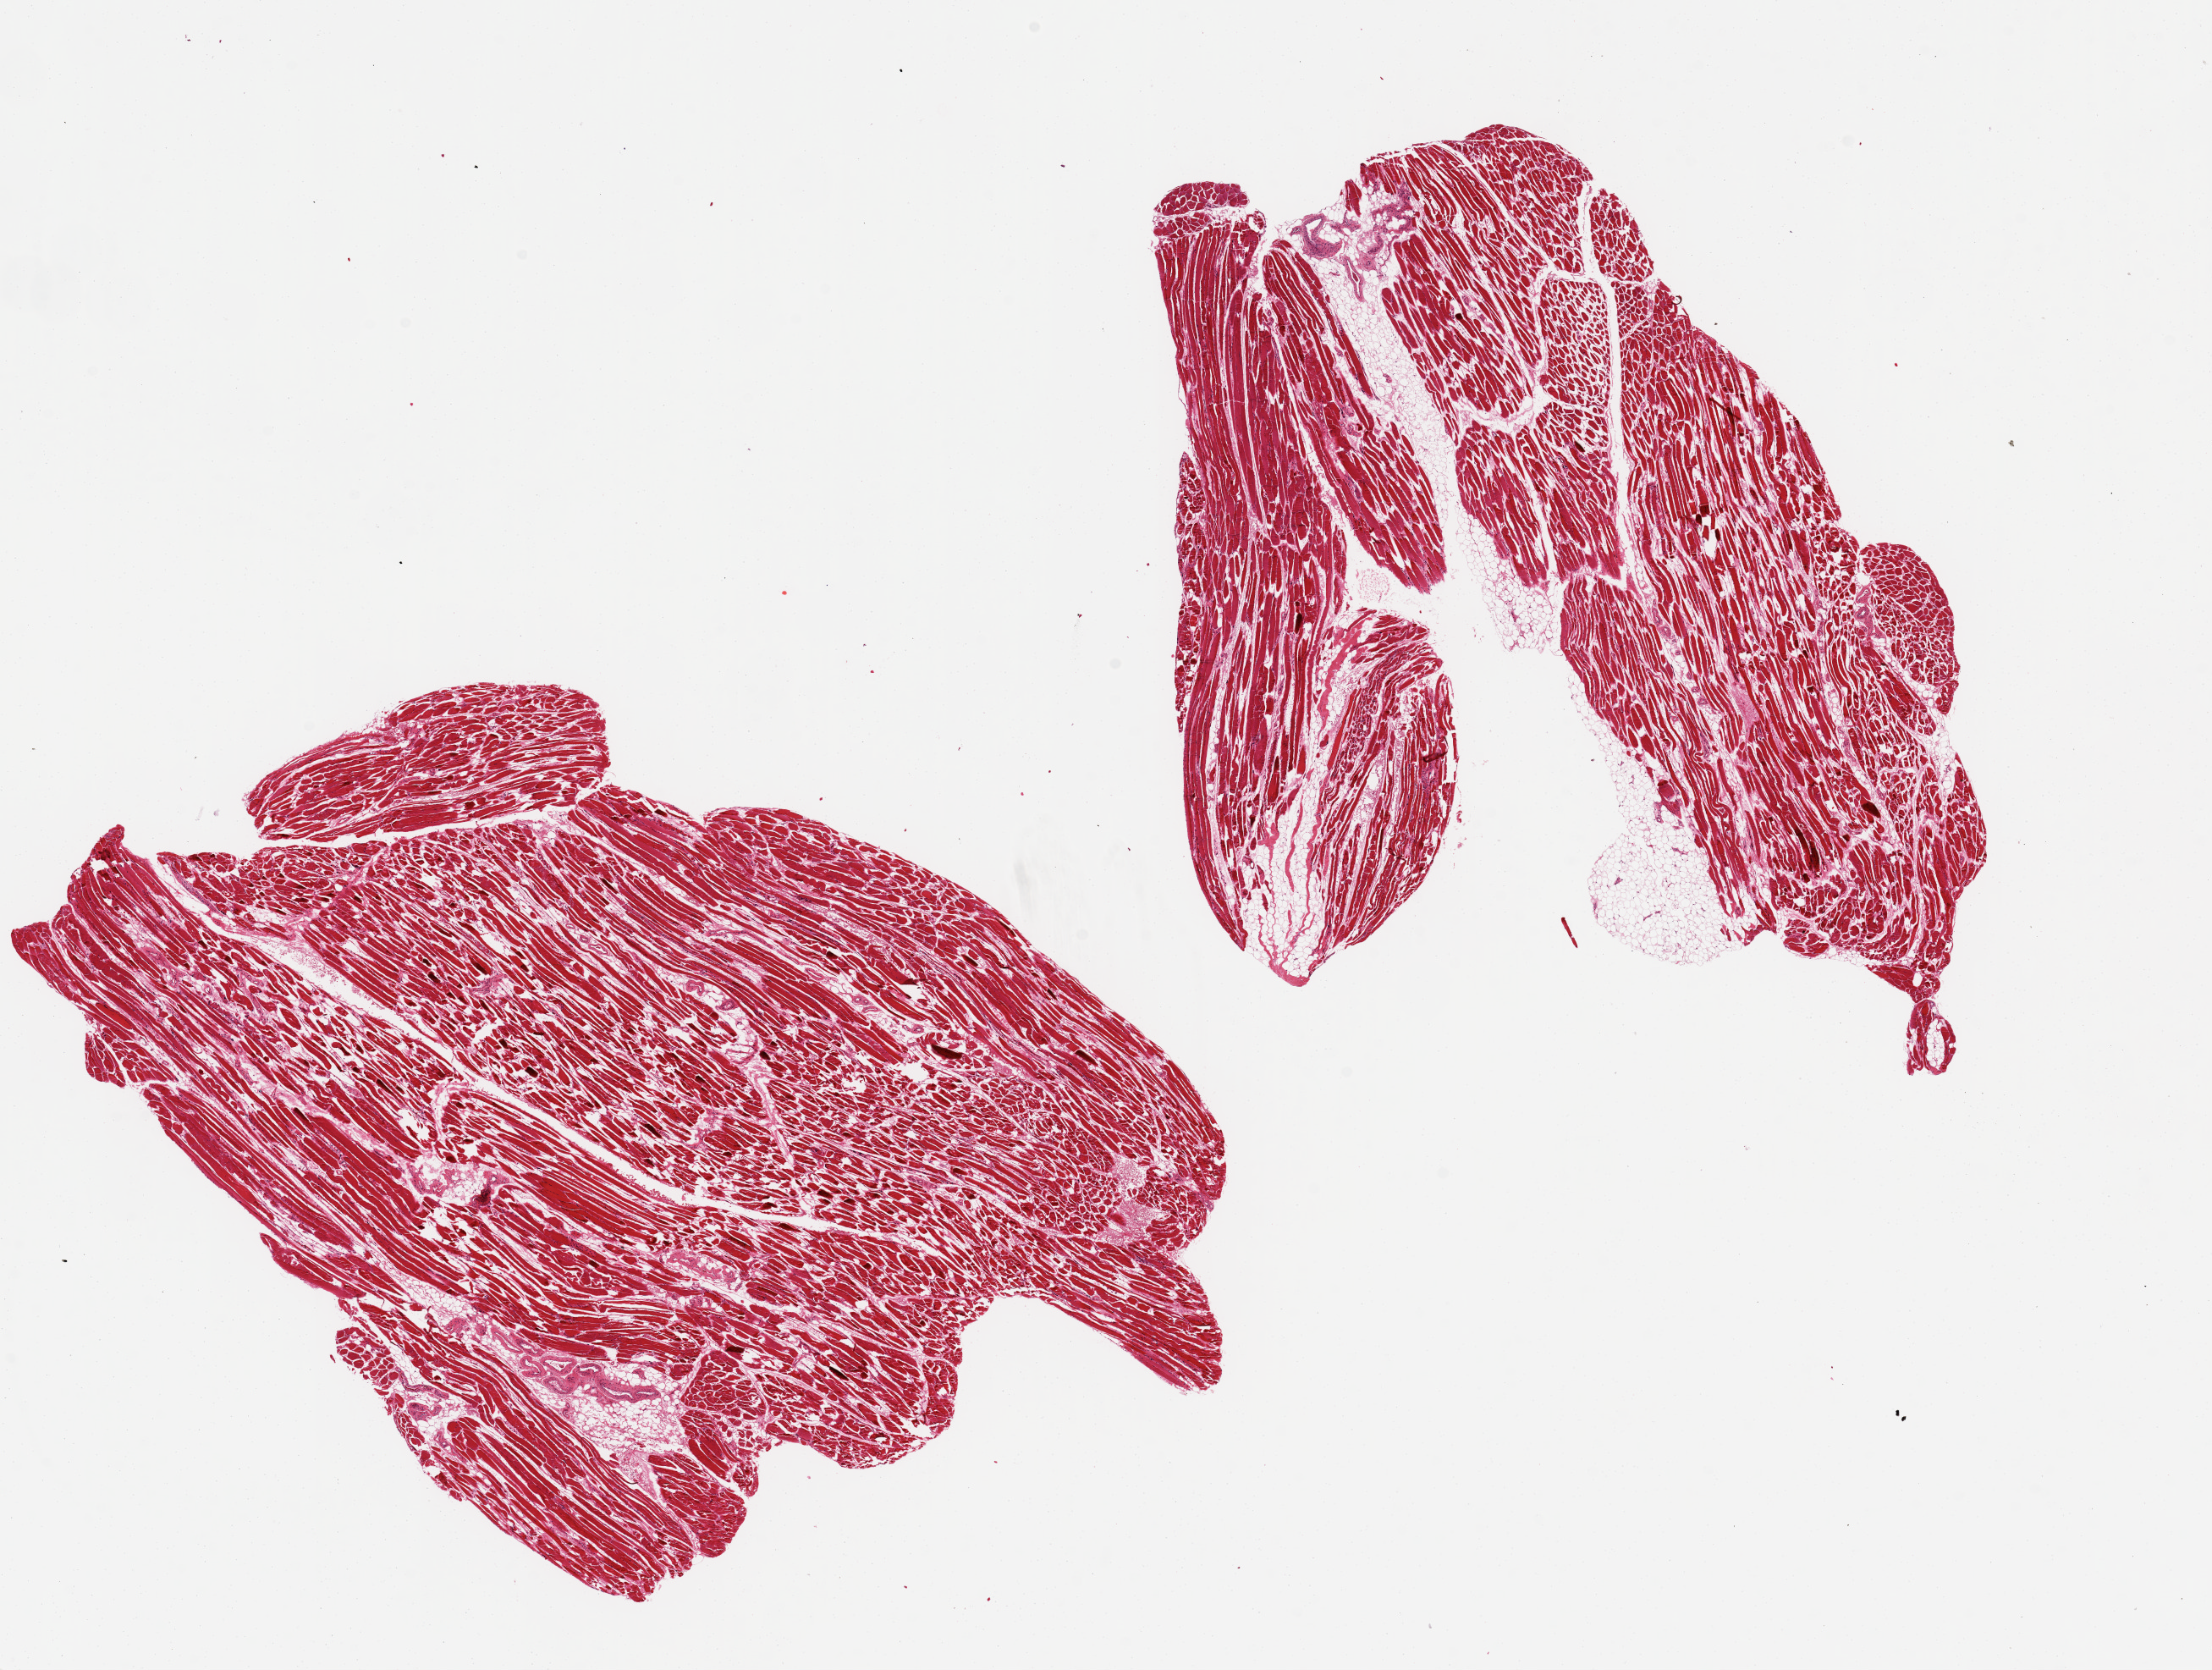
Haematoxylin and eosin whole-slide image, whole scanned area (about 20.7 x 15.6 mm, slide scanned at 20x) shown as a low-resolution overview. PAXgene-fixed paraffin-embedded (PFPE) section. Section of skeletal muscle (target tissue). Tissue donor sample. Donor: female.
Pathologist's review note for this sample: 2 pieces, both 9x7 mm.